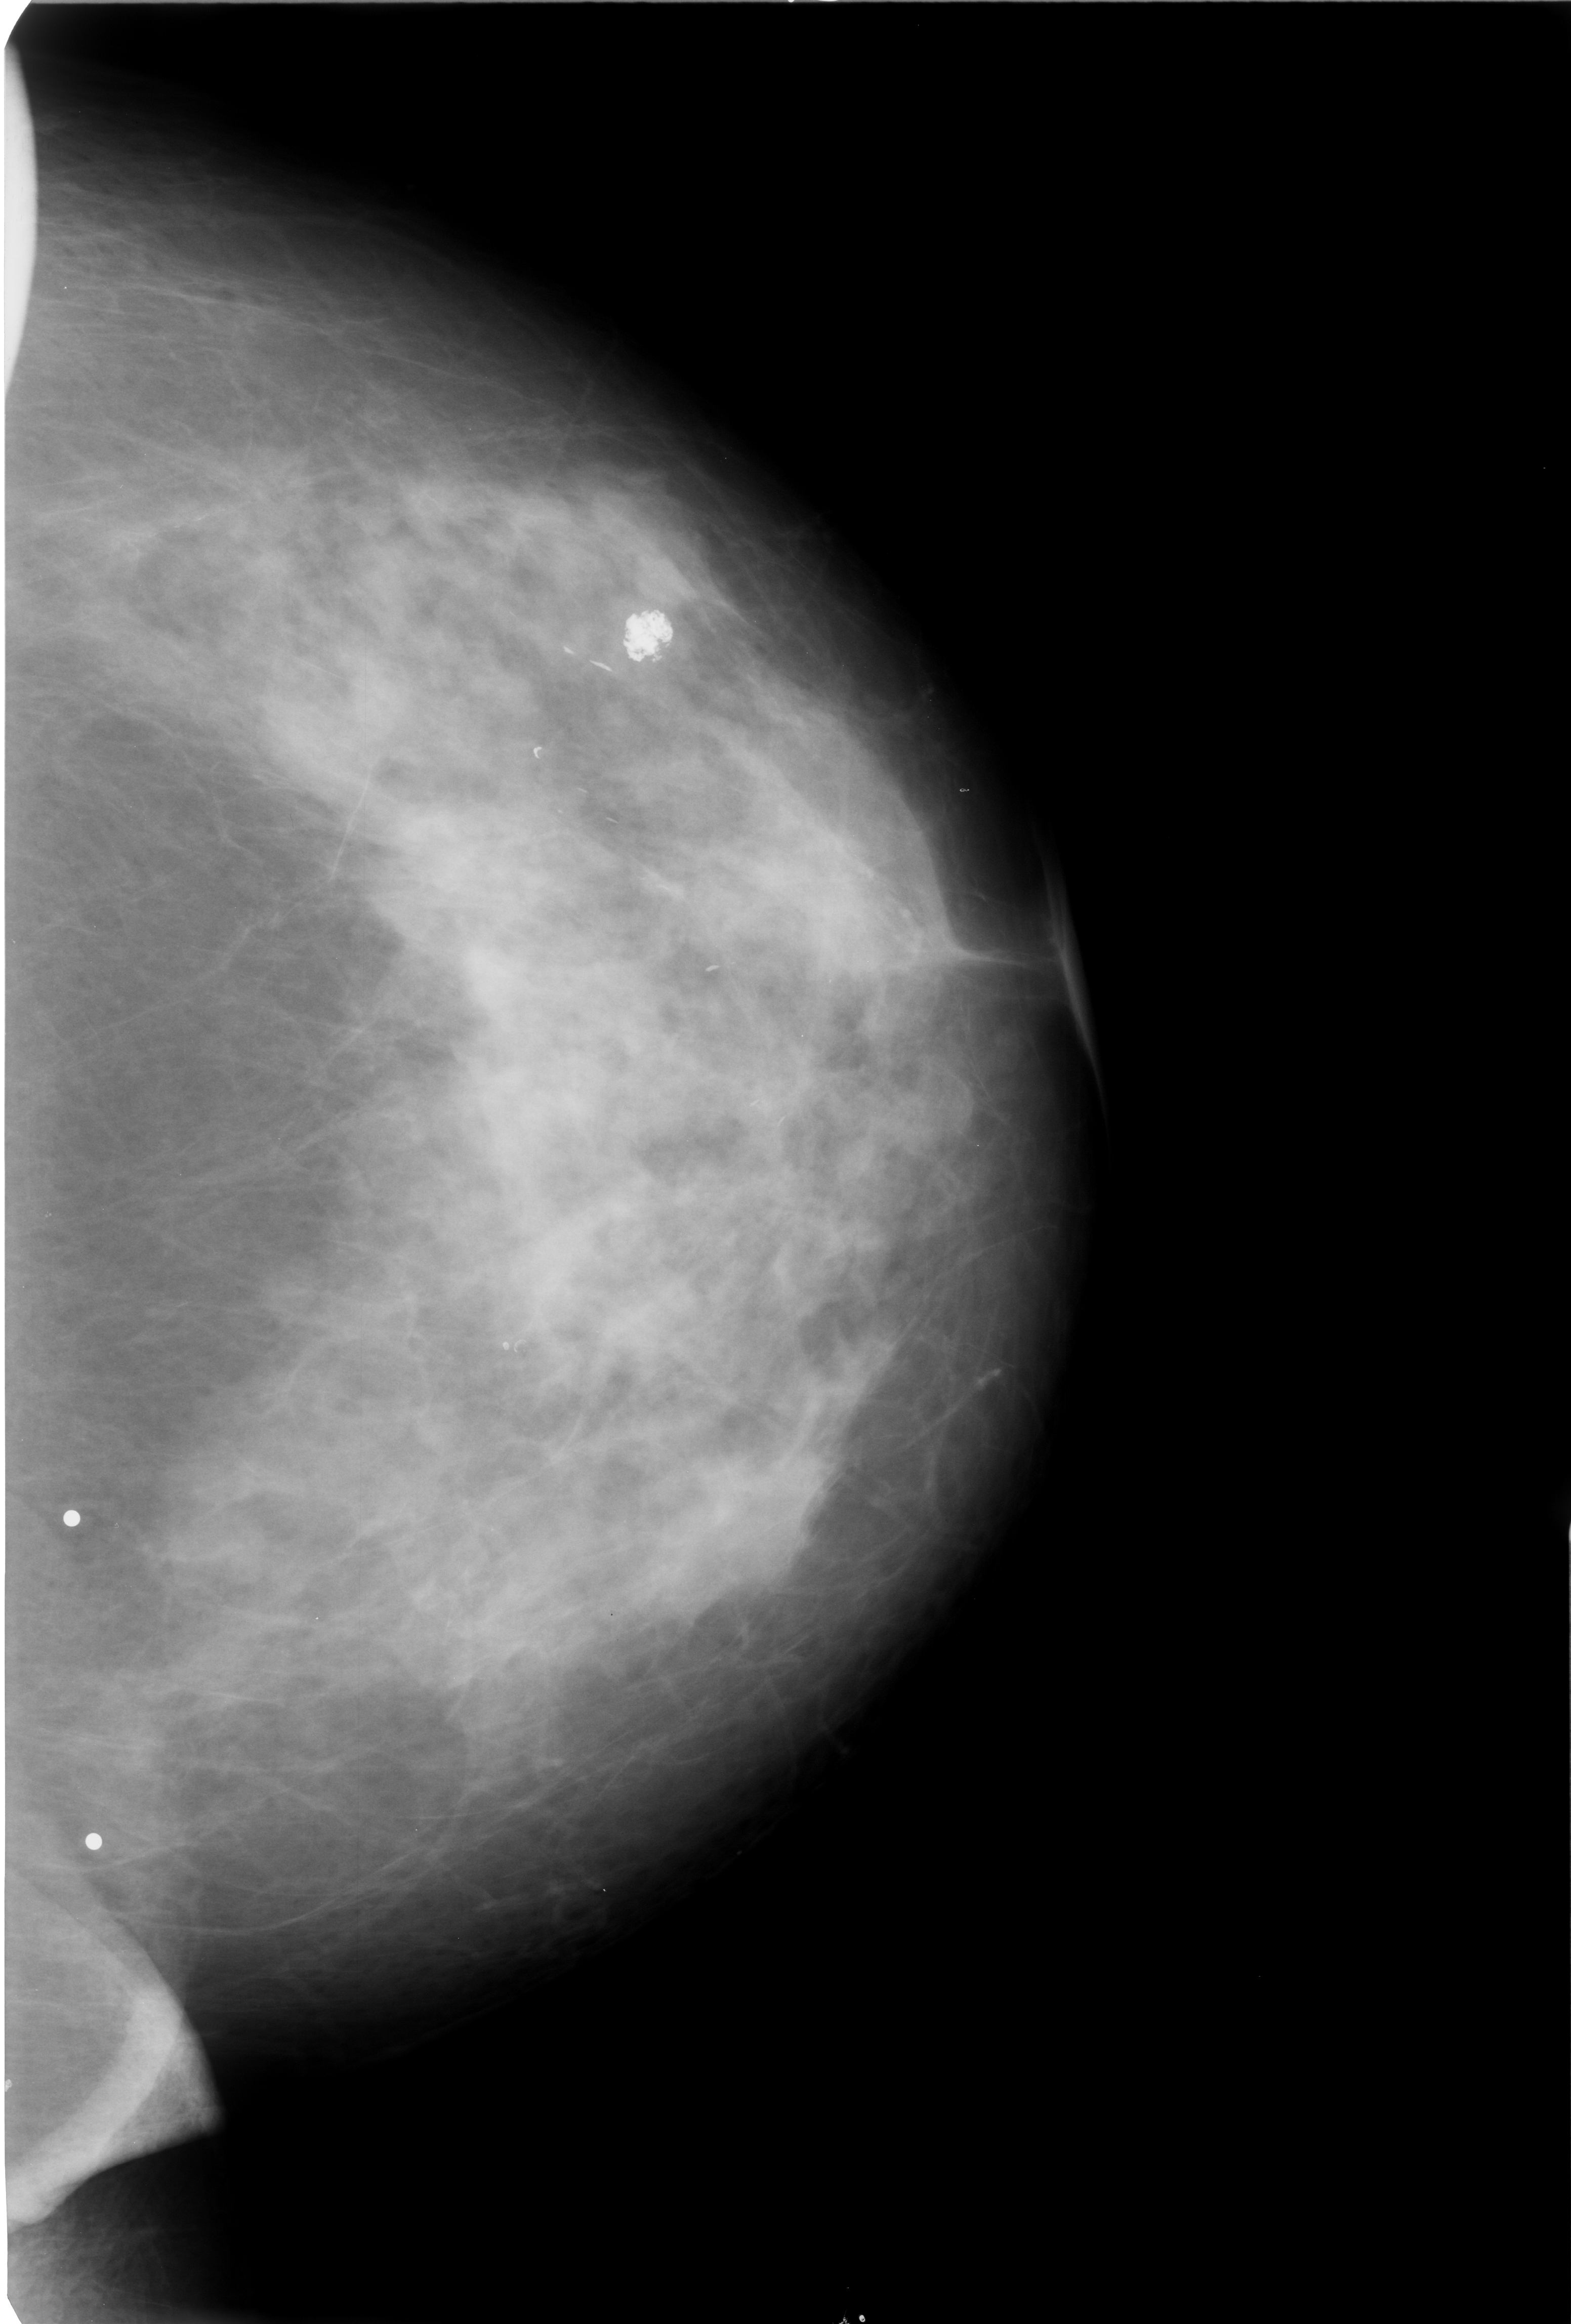
Mammogram (digitized film); left breast; CC view; BI-RADS breast density category 3 (scale 1–4); 1571 × 2324 image matrix.
Expert-marked regions of interest on this image (one box per marked abnormality):
- calcifications, distribution linear; BI-RADS assessment category 2; benign; no additional work-up was recommended (outcome (as recorded, no biopsy): benign without callback): box from (x=623, y=611) to (x=669, y=661) px